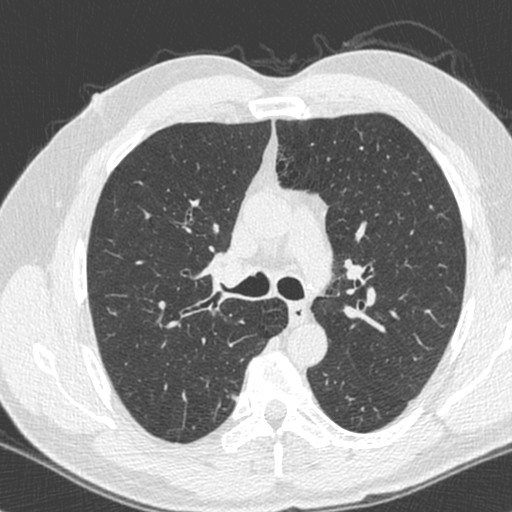
Chest CT (low-dose screening protocol), one axial image, baseline screening round, lung window (W 1500 / L -600 HU), slice 78 of 244 in the series, 512 × 512 image matrix, field of view 319 × 319 mm. Male participant, aged 55 years at enrolment.
Expert reader's lesion annotation, bounding box <218,383,247,409> (left, top, right, bottom; pixels). Screening reader's record for this exam: no non-calcified nodule ≥4 mm recorded. Official screen result: negative screen, minor abnormalities not suspicious for lung cancer. Later outcome: lung cancer diagnosed 1039 days after this screen (after the third annual screen) — adenocarcinoma, NOS, right upper lobe, poorly differentiated (G3), stage IA (AJCC 6th edition), 15 mm at pathology.